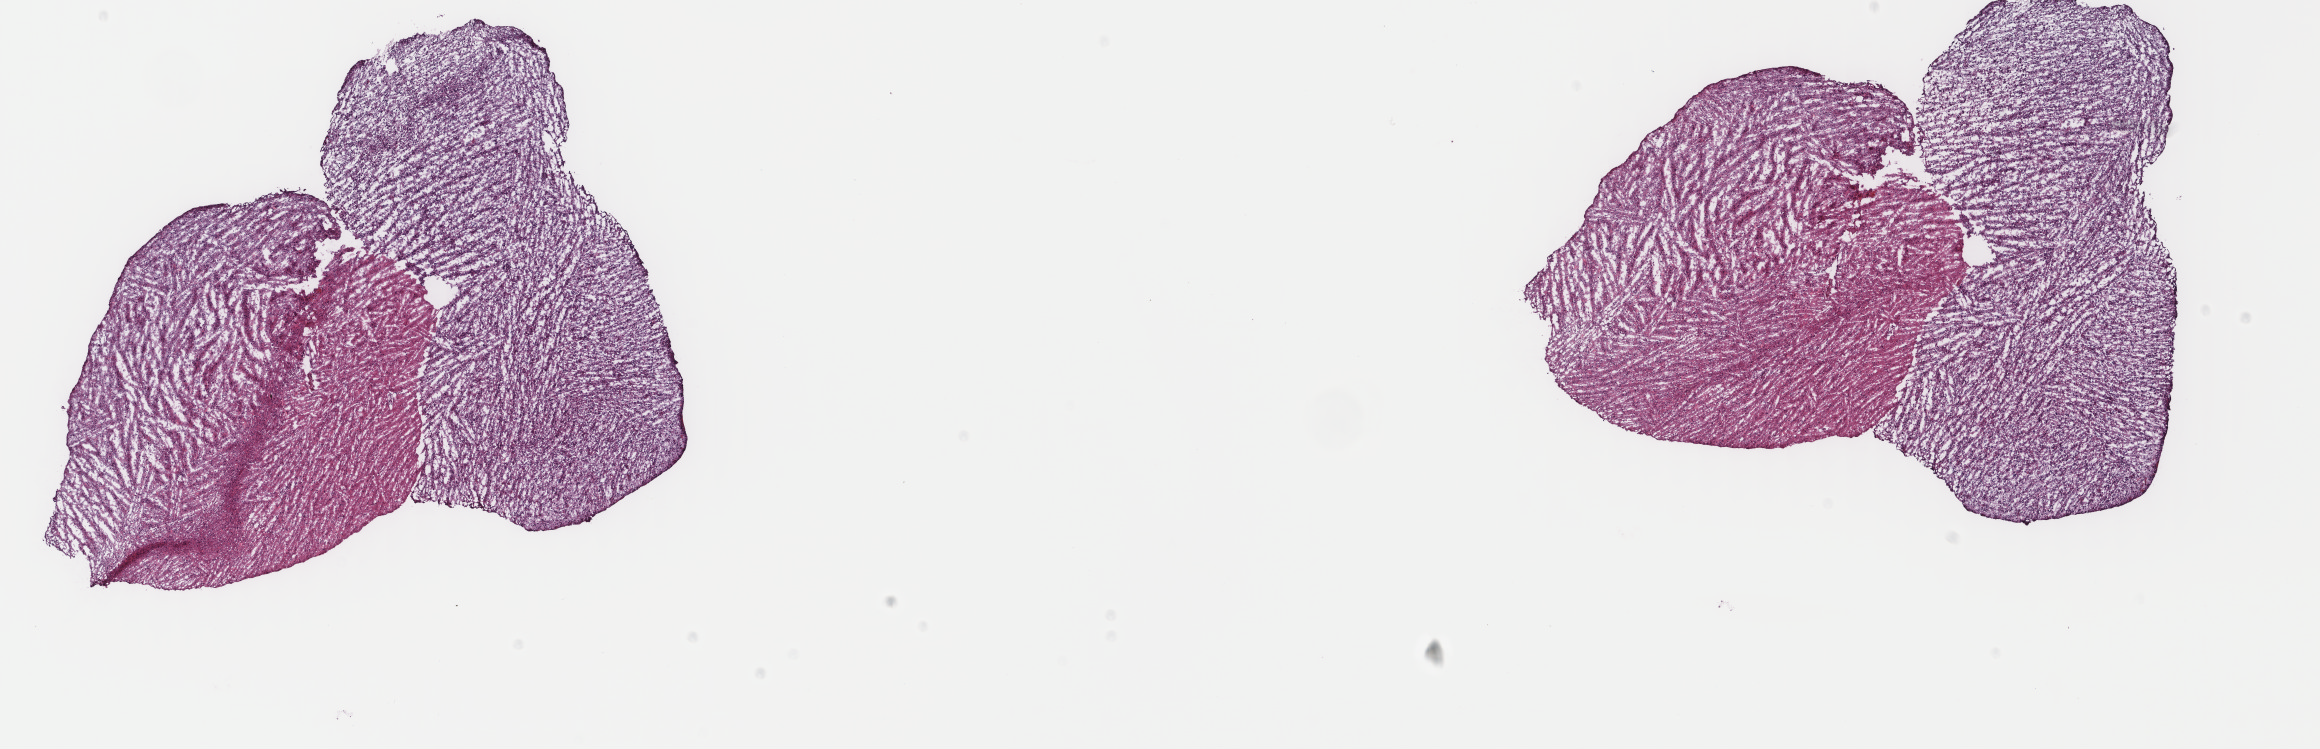
Digitized H&E-stained tissue section (whole slide), whole scanned area (about 18.4 x 5.9 mm, slide scanned at 40x) shown as a low-resolution overview, frozen section, primary tumour sample from the brain. Female patient; age at initial diagnosis 46 years. Histologic grade: G3 (poorly differentiated). Slide review estimates, as recorded: tumour cells 80%, tumour nuclei 90%, normal cells 10%, stromal cells 10%, necrosis 0%. Inflammatory infiltration, as recorded: lymphocyte infiltration 0%, monocyte infiltration 0%, neutrophil infiltration 0%.
Laterality: left. Pathologic diagnosis: Astrocytoma, anaplastic (cerebrum).